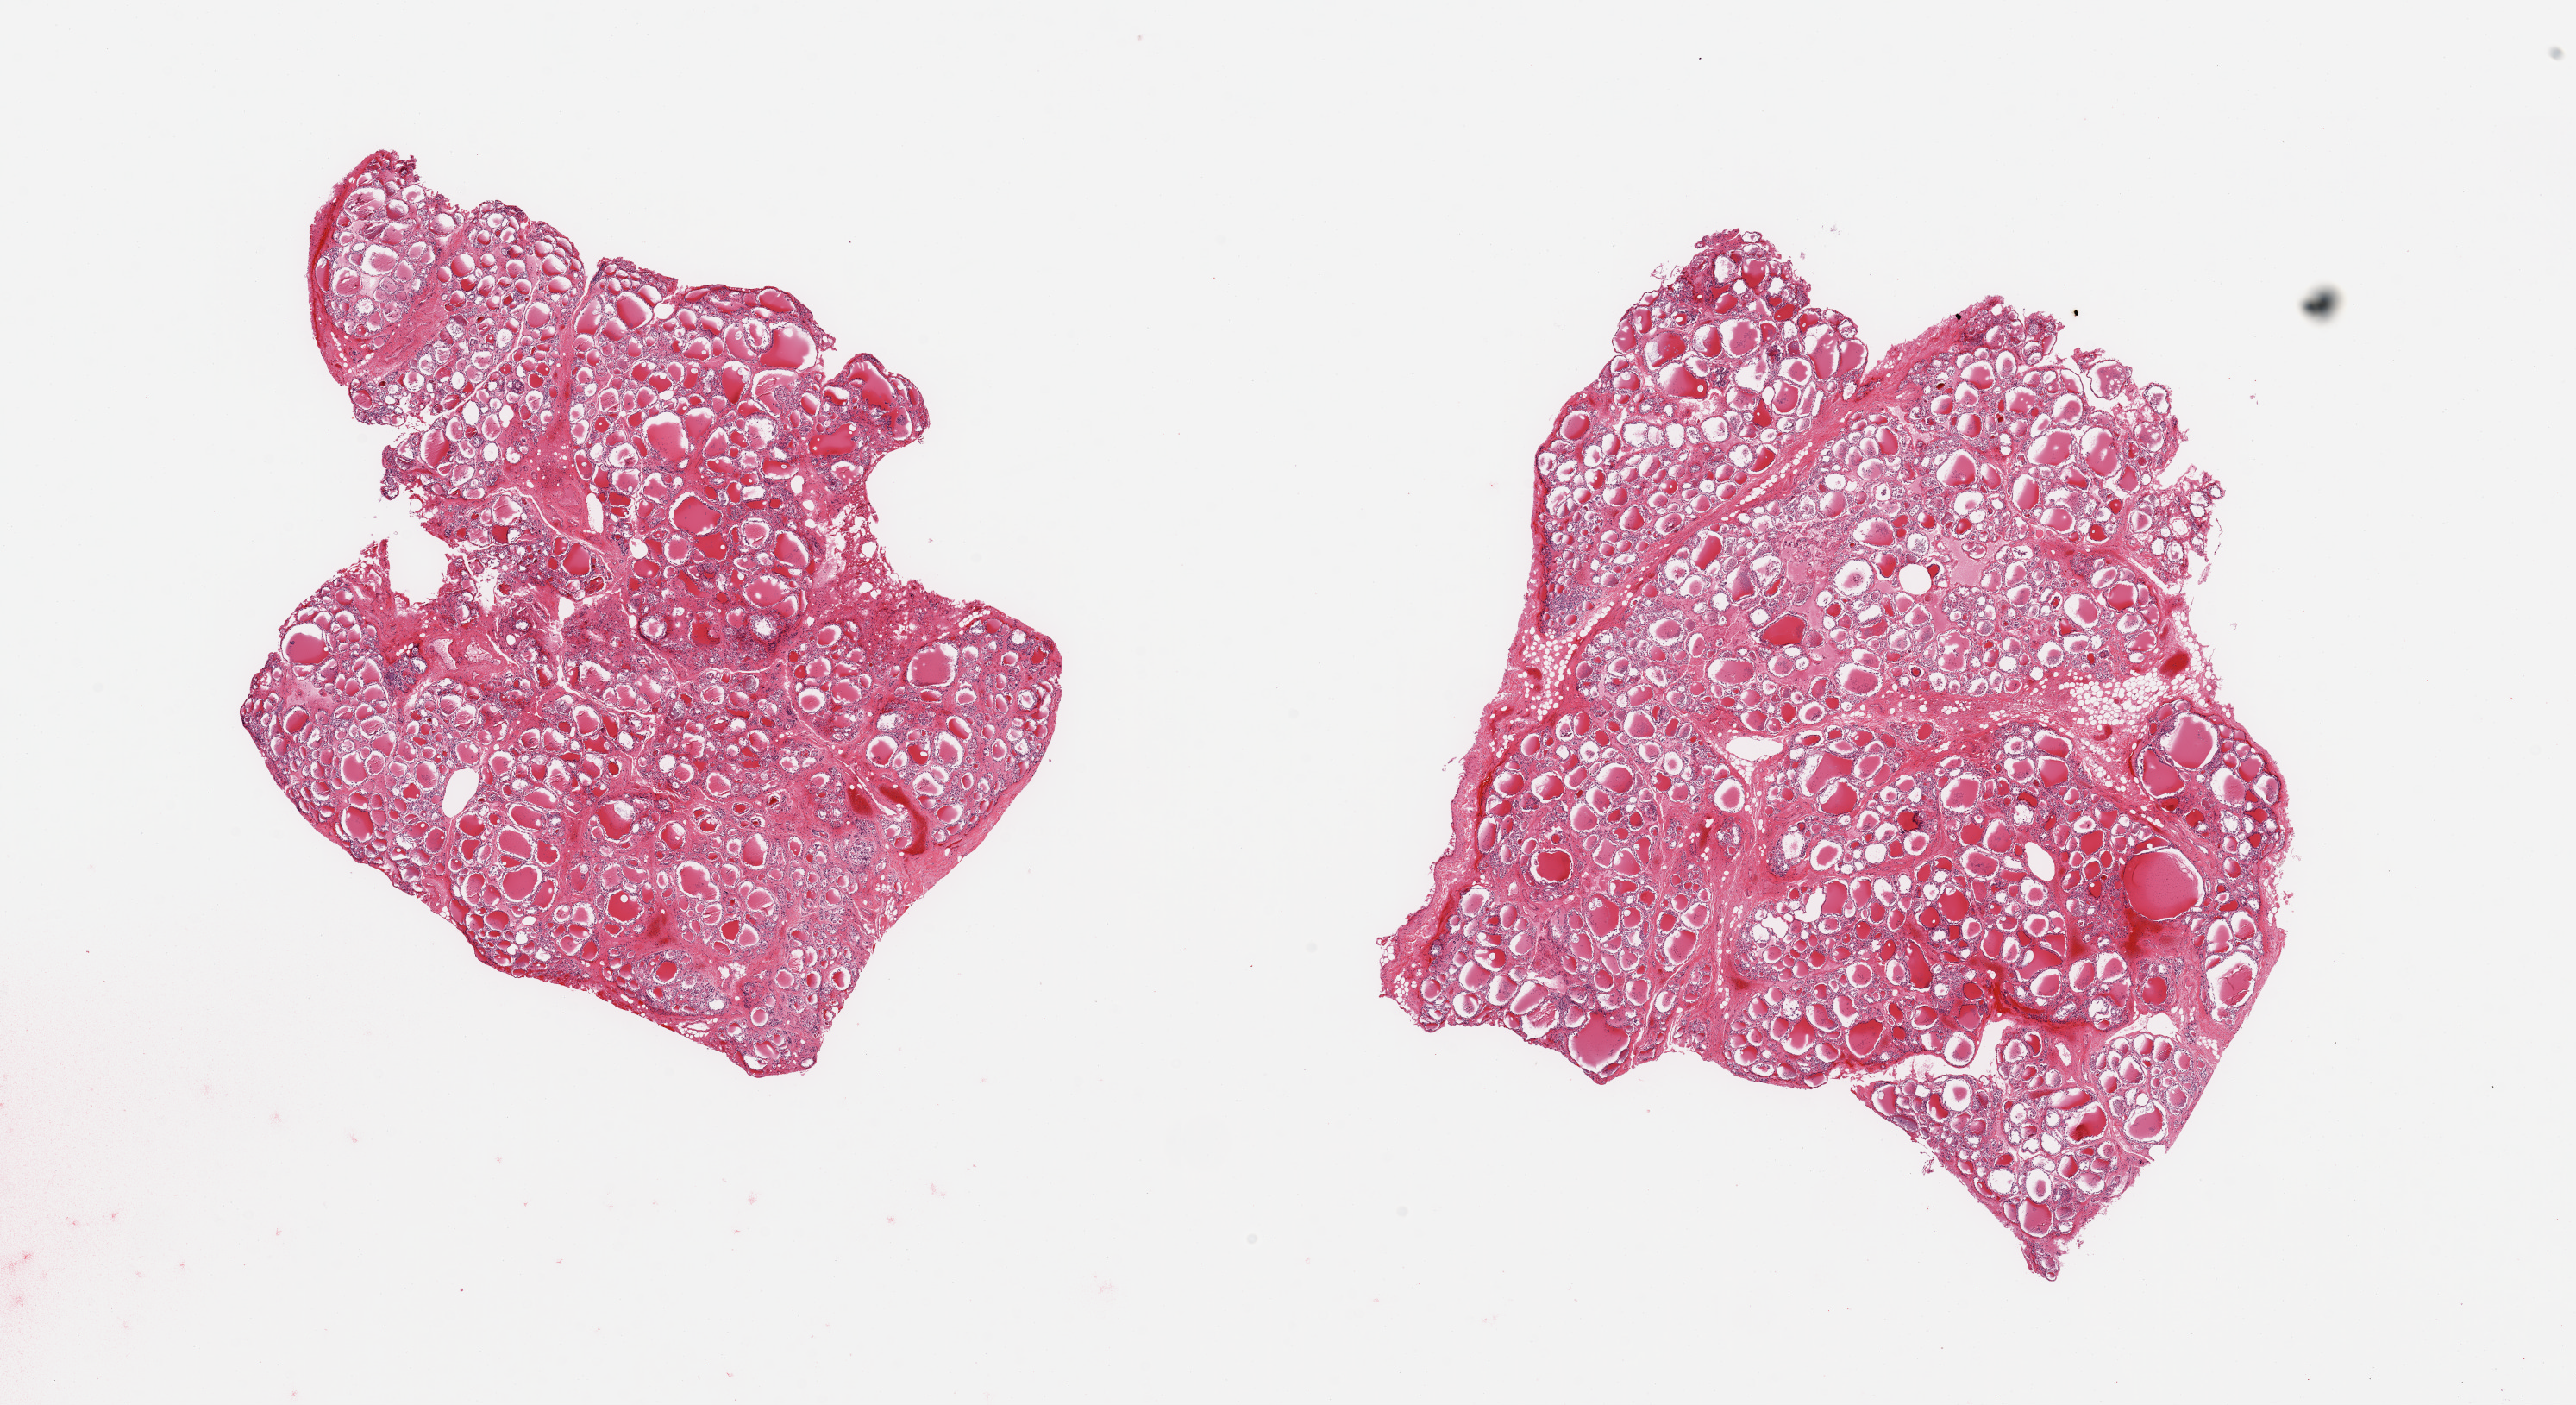
Digitized hematoxylin and eosin (H&E)-stained section, low-resolution overview of the scanned area, about 23.6 x 12.9 mm (slide scanned at 20x). PAXgene-fixed, paraffin-embedded tissue. Target tissue: thyroid. Tissue donor sample. Donor sex: male.
Pathologist's review note for this sample: 2 pieces; no lesions.